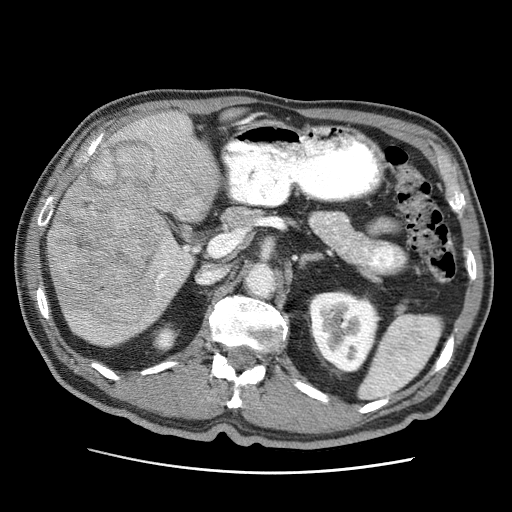
Contrast-enhanced abdominal CT (liver protocol), one axial slice. Soft-tissue window (W 400 / L 40 HU). 2.5 mm slice thickness. 512 × 512 image matrix, field of view 360 × 360 mm. From the clinical record (not read from this slice): diagnosis: hepatocellular carcinoma (patient treated with transarterial chemoembolisation; whether this scan precedes or follows treatment is not stated here); TNM stage (as recorded): Stage-IIIA; Child-Pugh class: A; tumour differentiation: well differentiated.
Structures marked on this image (semi-automatically segmented with operator editing):
- liver parenchyma outside the tumour (the mass and vessels are separate outlines, so this box may not span the whole liver): bounding box <46,111,218,346> (left, top, right, bottom; pixels)
- mass: <49,140,198,324>
- liver vessels: <69,121,188,324>